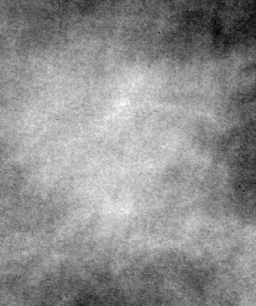
Region of interest cut from a scanned film mammogram (one marked finding); left breast; CC view; BI-RADS breast density category 2 (scale 1–4).
- Finding: mass, shape irregular, margins spiculated; BI-RADS assessment category 4; subtlety rating 4 on a 1 (subtle) to 5 (obvious) scale; pathology result (as recorded, not read from the image): malignant.